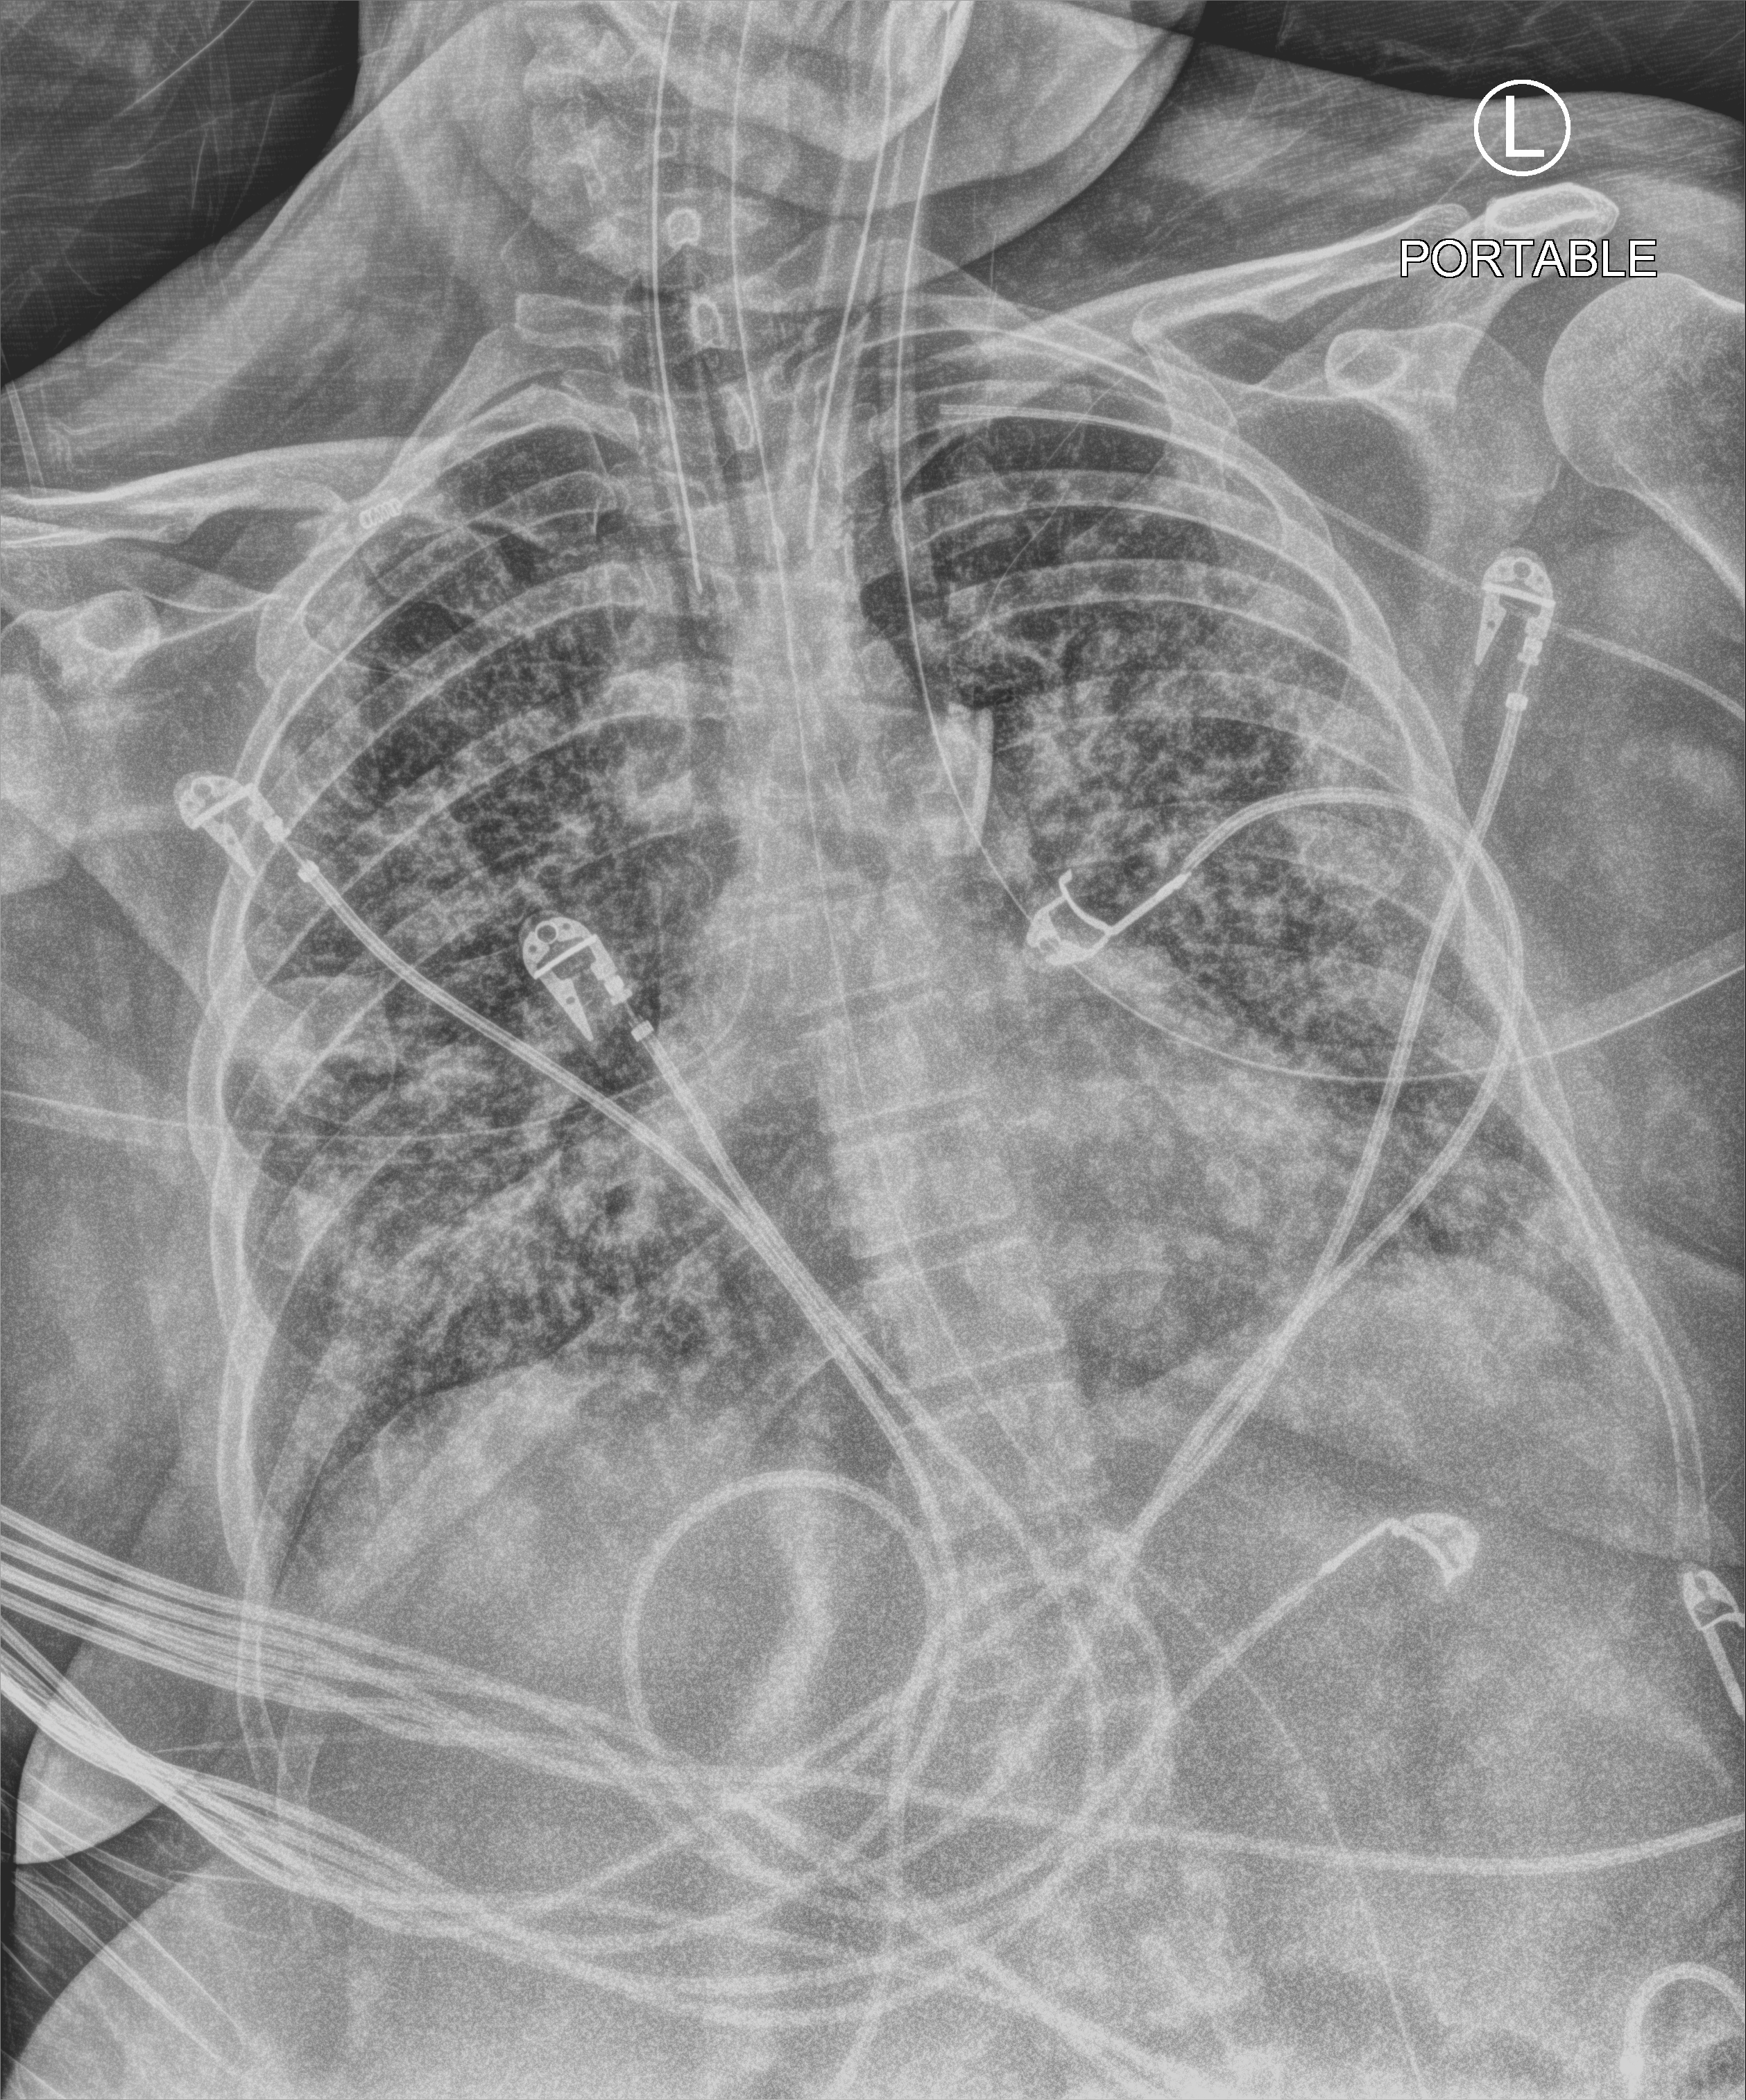
Chest X-ray (portable), anteroposterior (AP) projection. Patient hospitalised with COVID-19; female, aged 18–59 years.
Admission-level facts for this patient (not findings on this image; timing relative to this image not recorded): smoking status (admission record): never; mechanically ventilated during this hospital stay: yes.